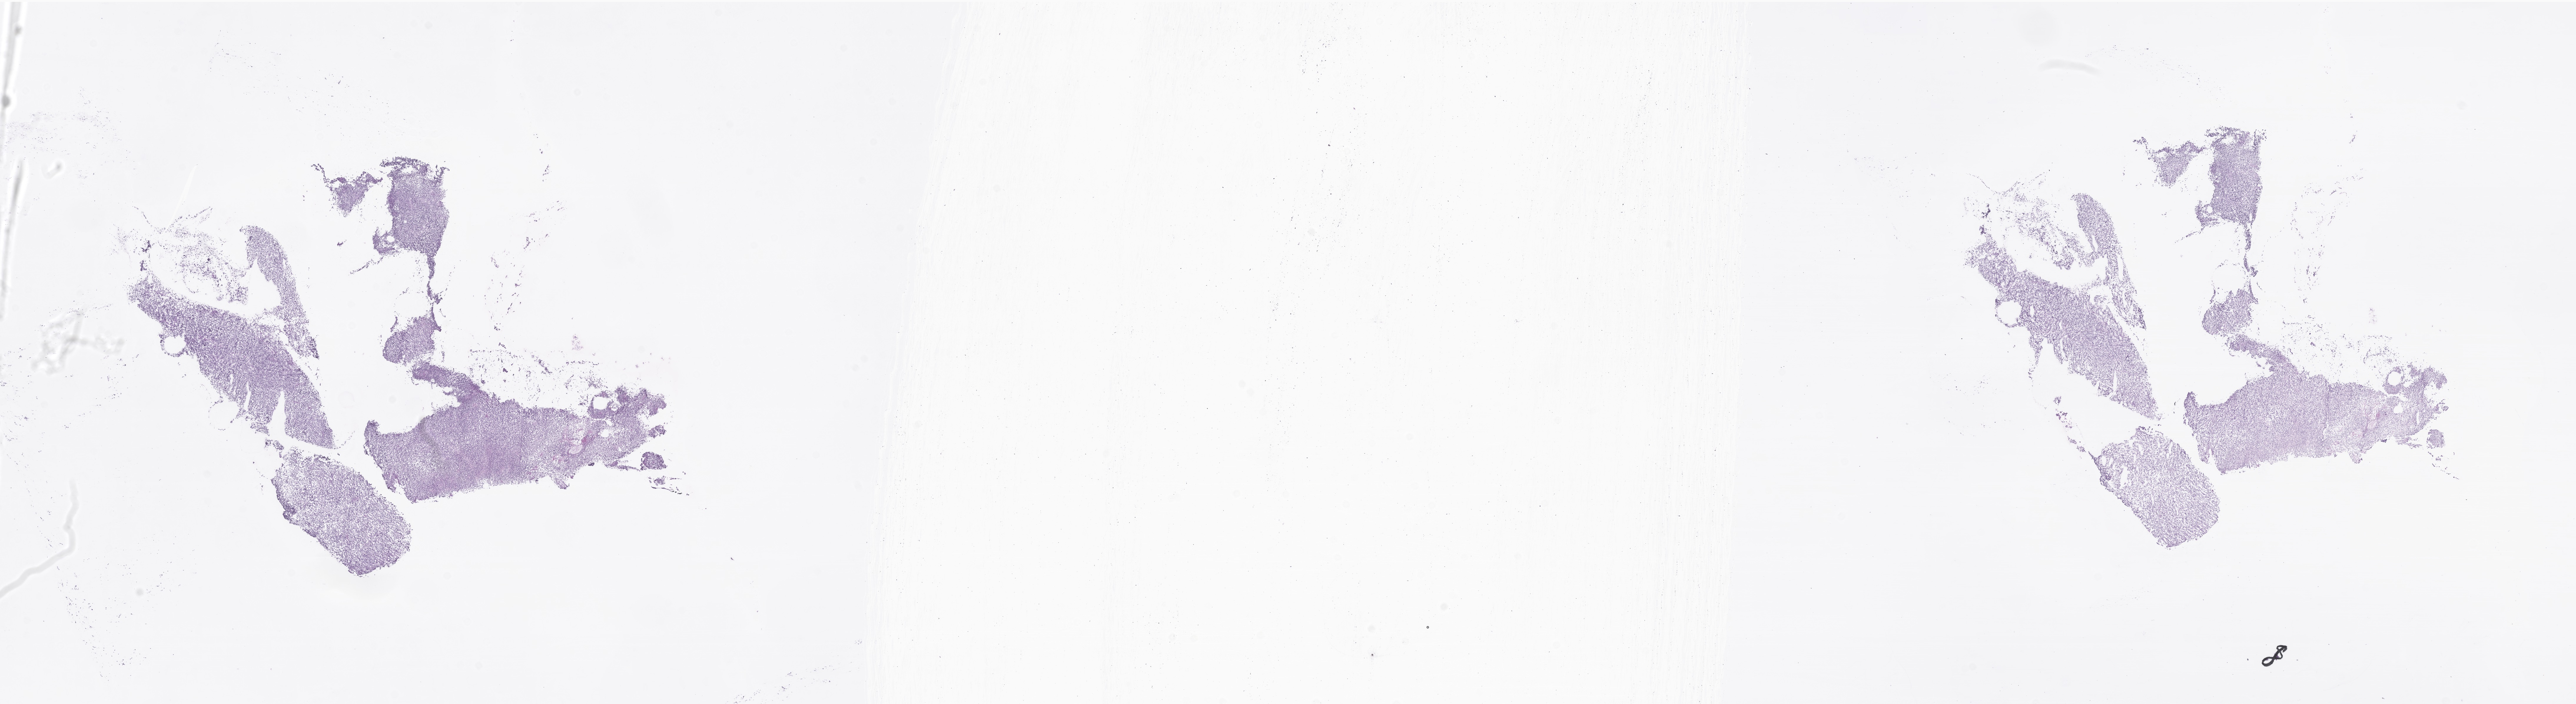
H&E whole-slide image of tumor tissue from the brain — whole scanned area (about 36.9 x 10.1 mm) shown as a low-resolution overview. Frozen section (OCT-embedded). Patient male; age 100 months (8 years 4 months).
Recorded diagnosis: Medulloblastoma, NOS.